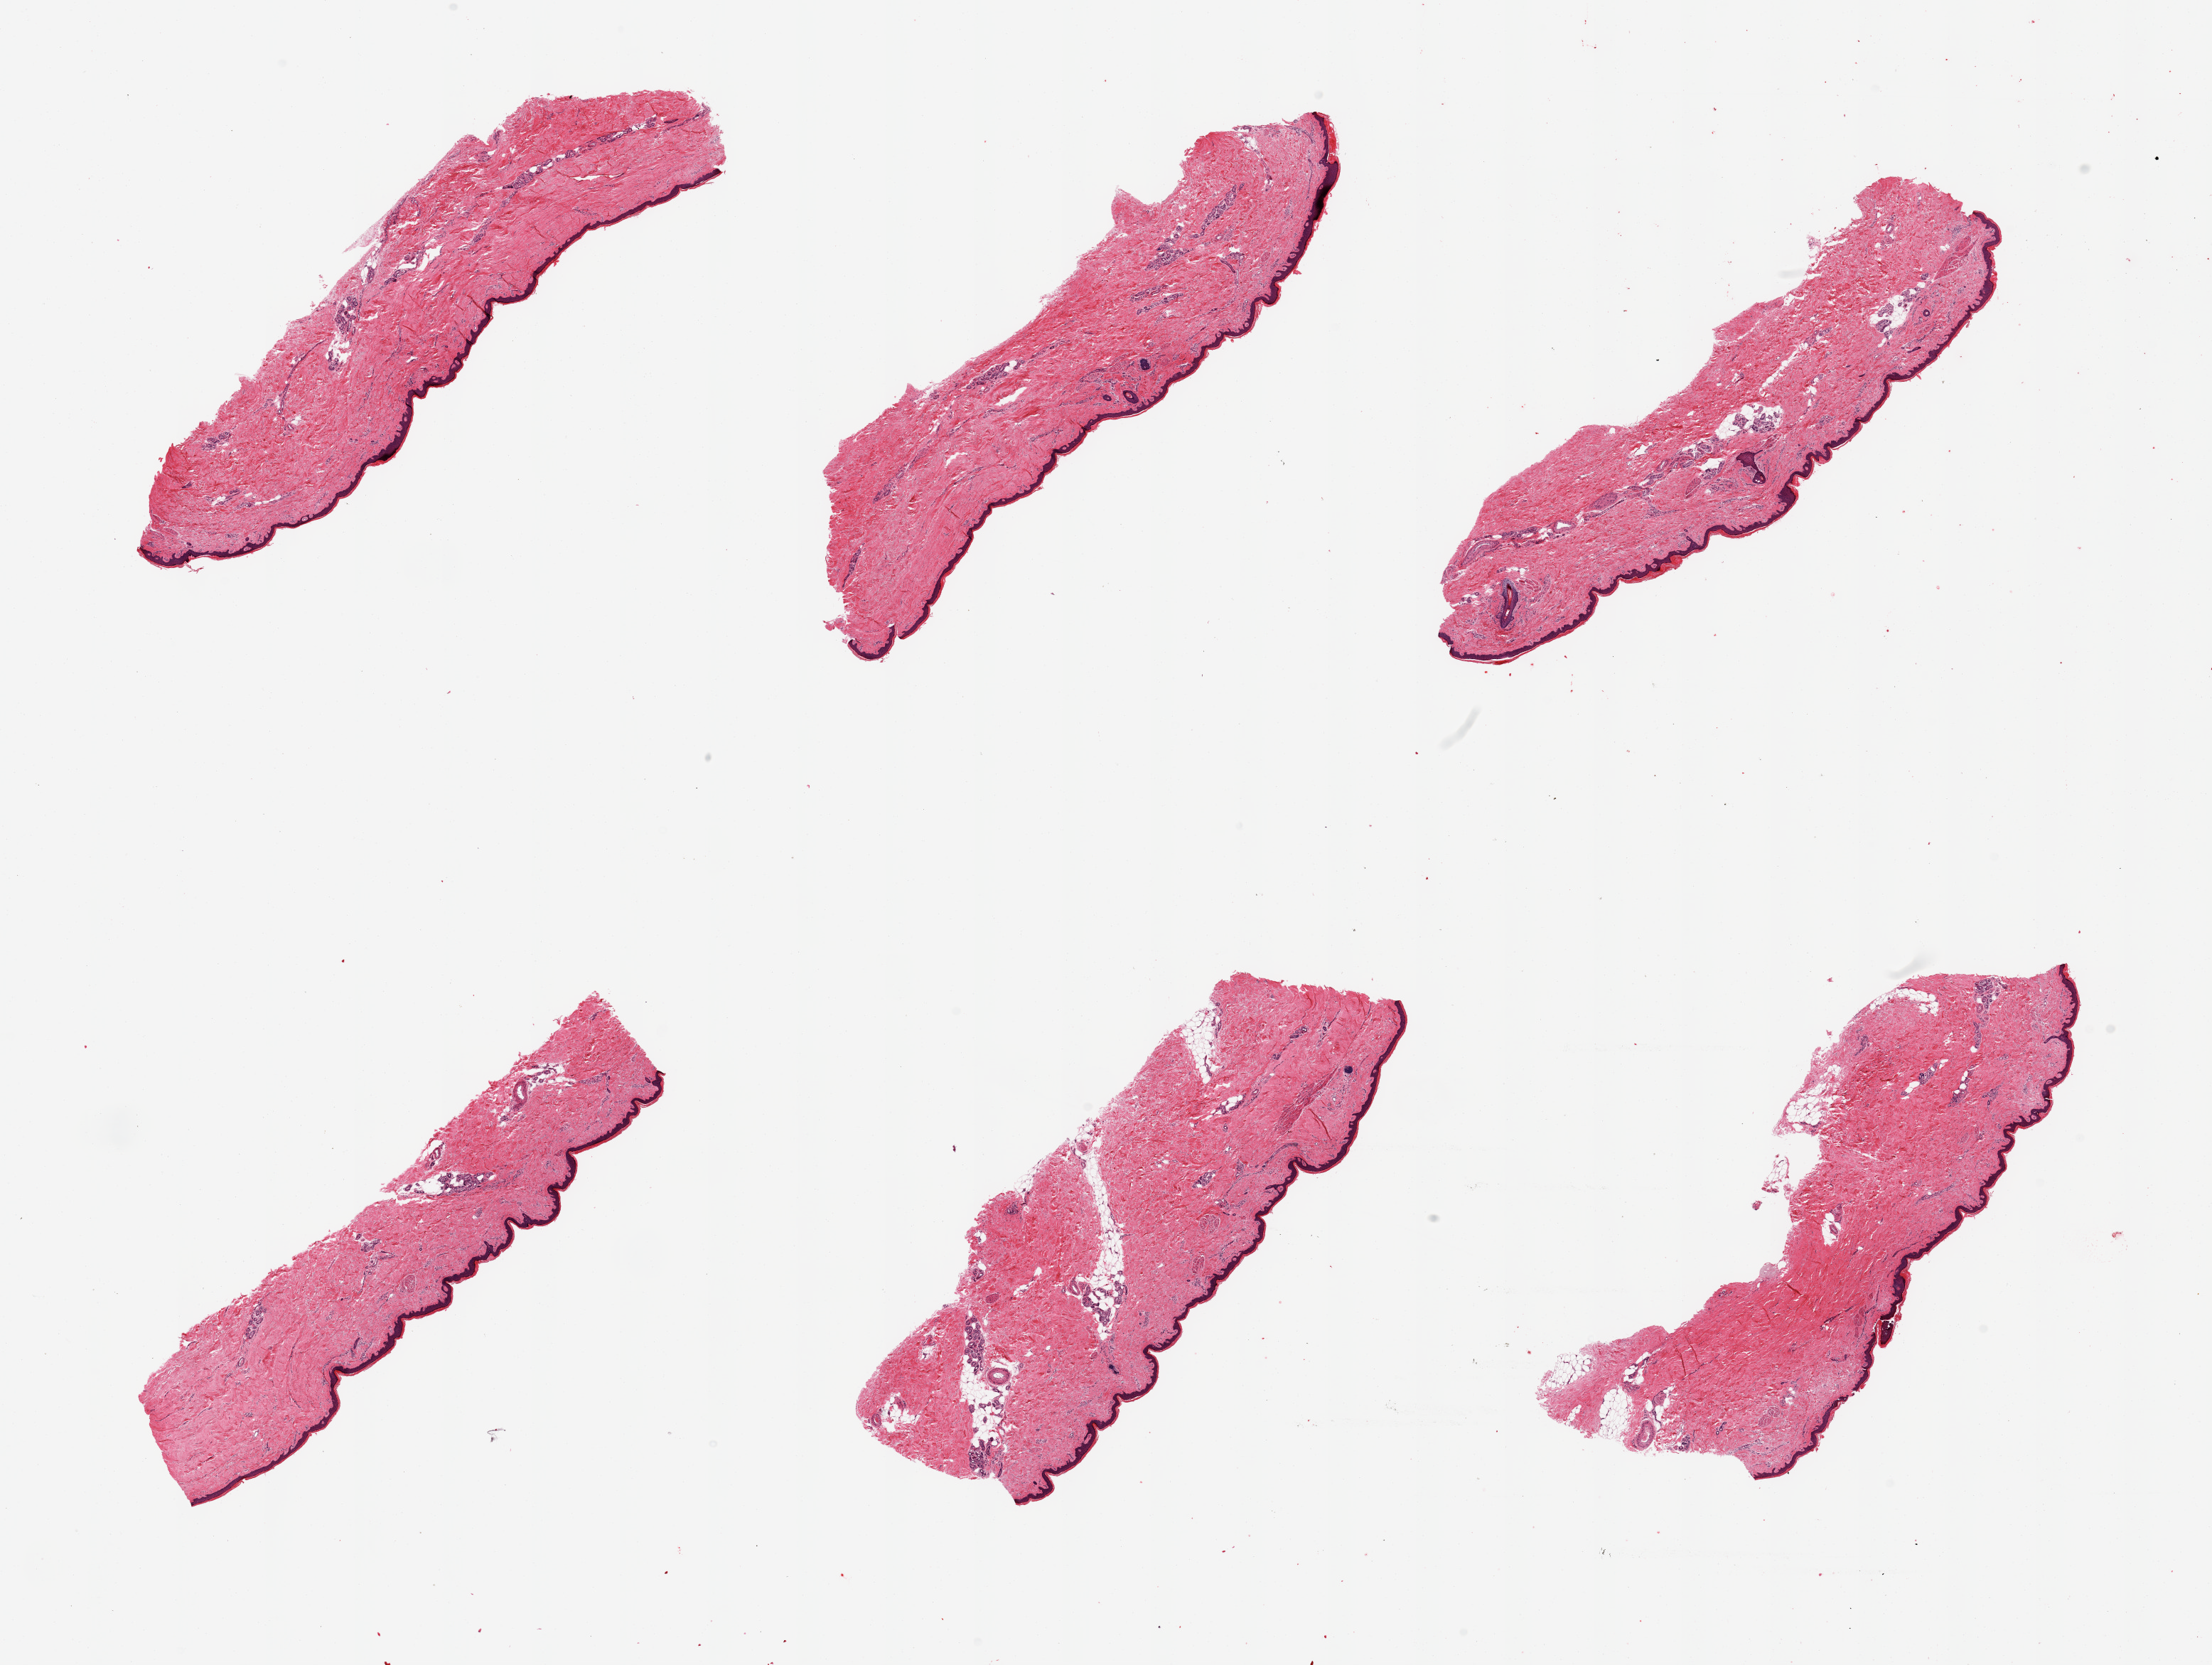
H&E whole-slide image, brightfield — whole scanned area (about 24.6 x 18.5 mm, slide scanned at 20x) shown as a low-resolution overview; PAXgene-fixed paraffin-embedded (PFPE) section; target tissue: skin of lower leg; tissue donor sample. Donor sex: male.
* pathologist's review note for this sample: 6 pieces; well trimmed; 5-10% dermall fat